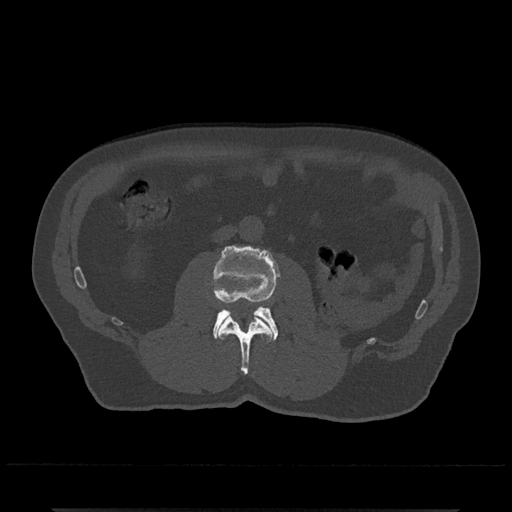
CT including the spine, one axial slice; position 257 of 797 along the scan axis; bone window (W 1800 / L 400 HU); 512 × 512 image matrix, field of view 393 × 393 mm. Patient: male, 67 years. From the clinical record (not read from this slice): primary cancer: prostate.
Outlined on this slice (semi-automatic segmentation, software-assisted and operator-edited):
- L2 vertebra: bounding box (x1, y1, x2, y2) in pixels: (218, 315, 273, 375)
- L3 vertebra: (207, 246, 280, 341)